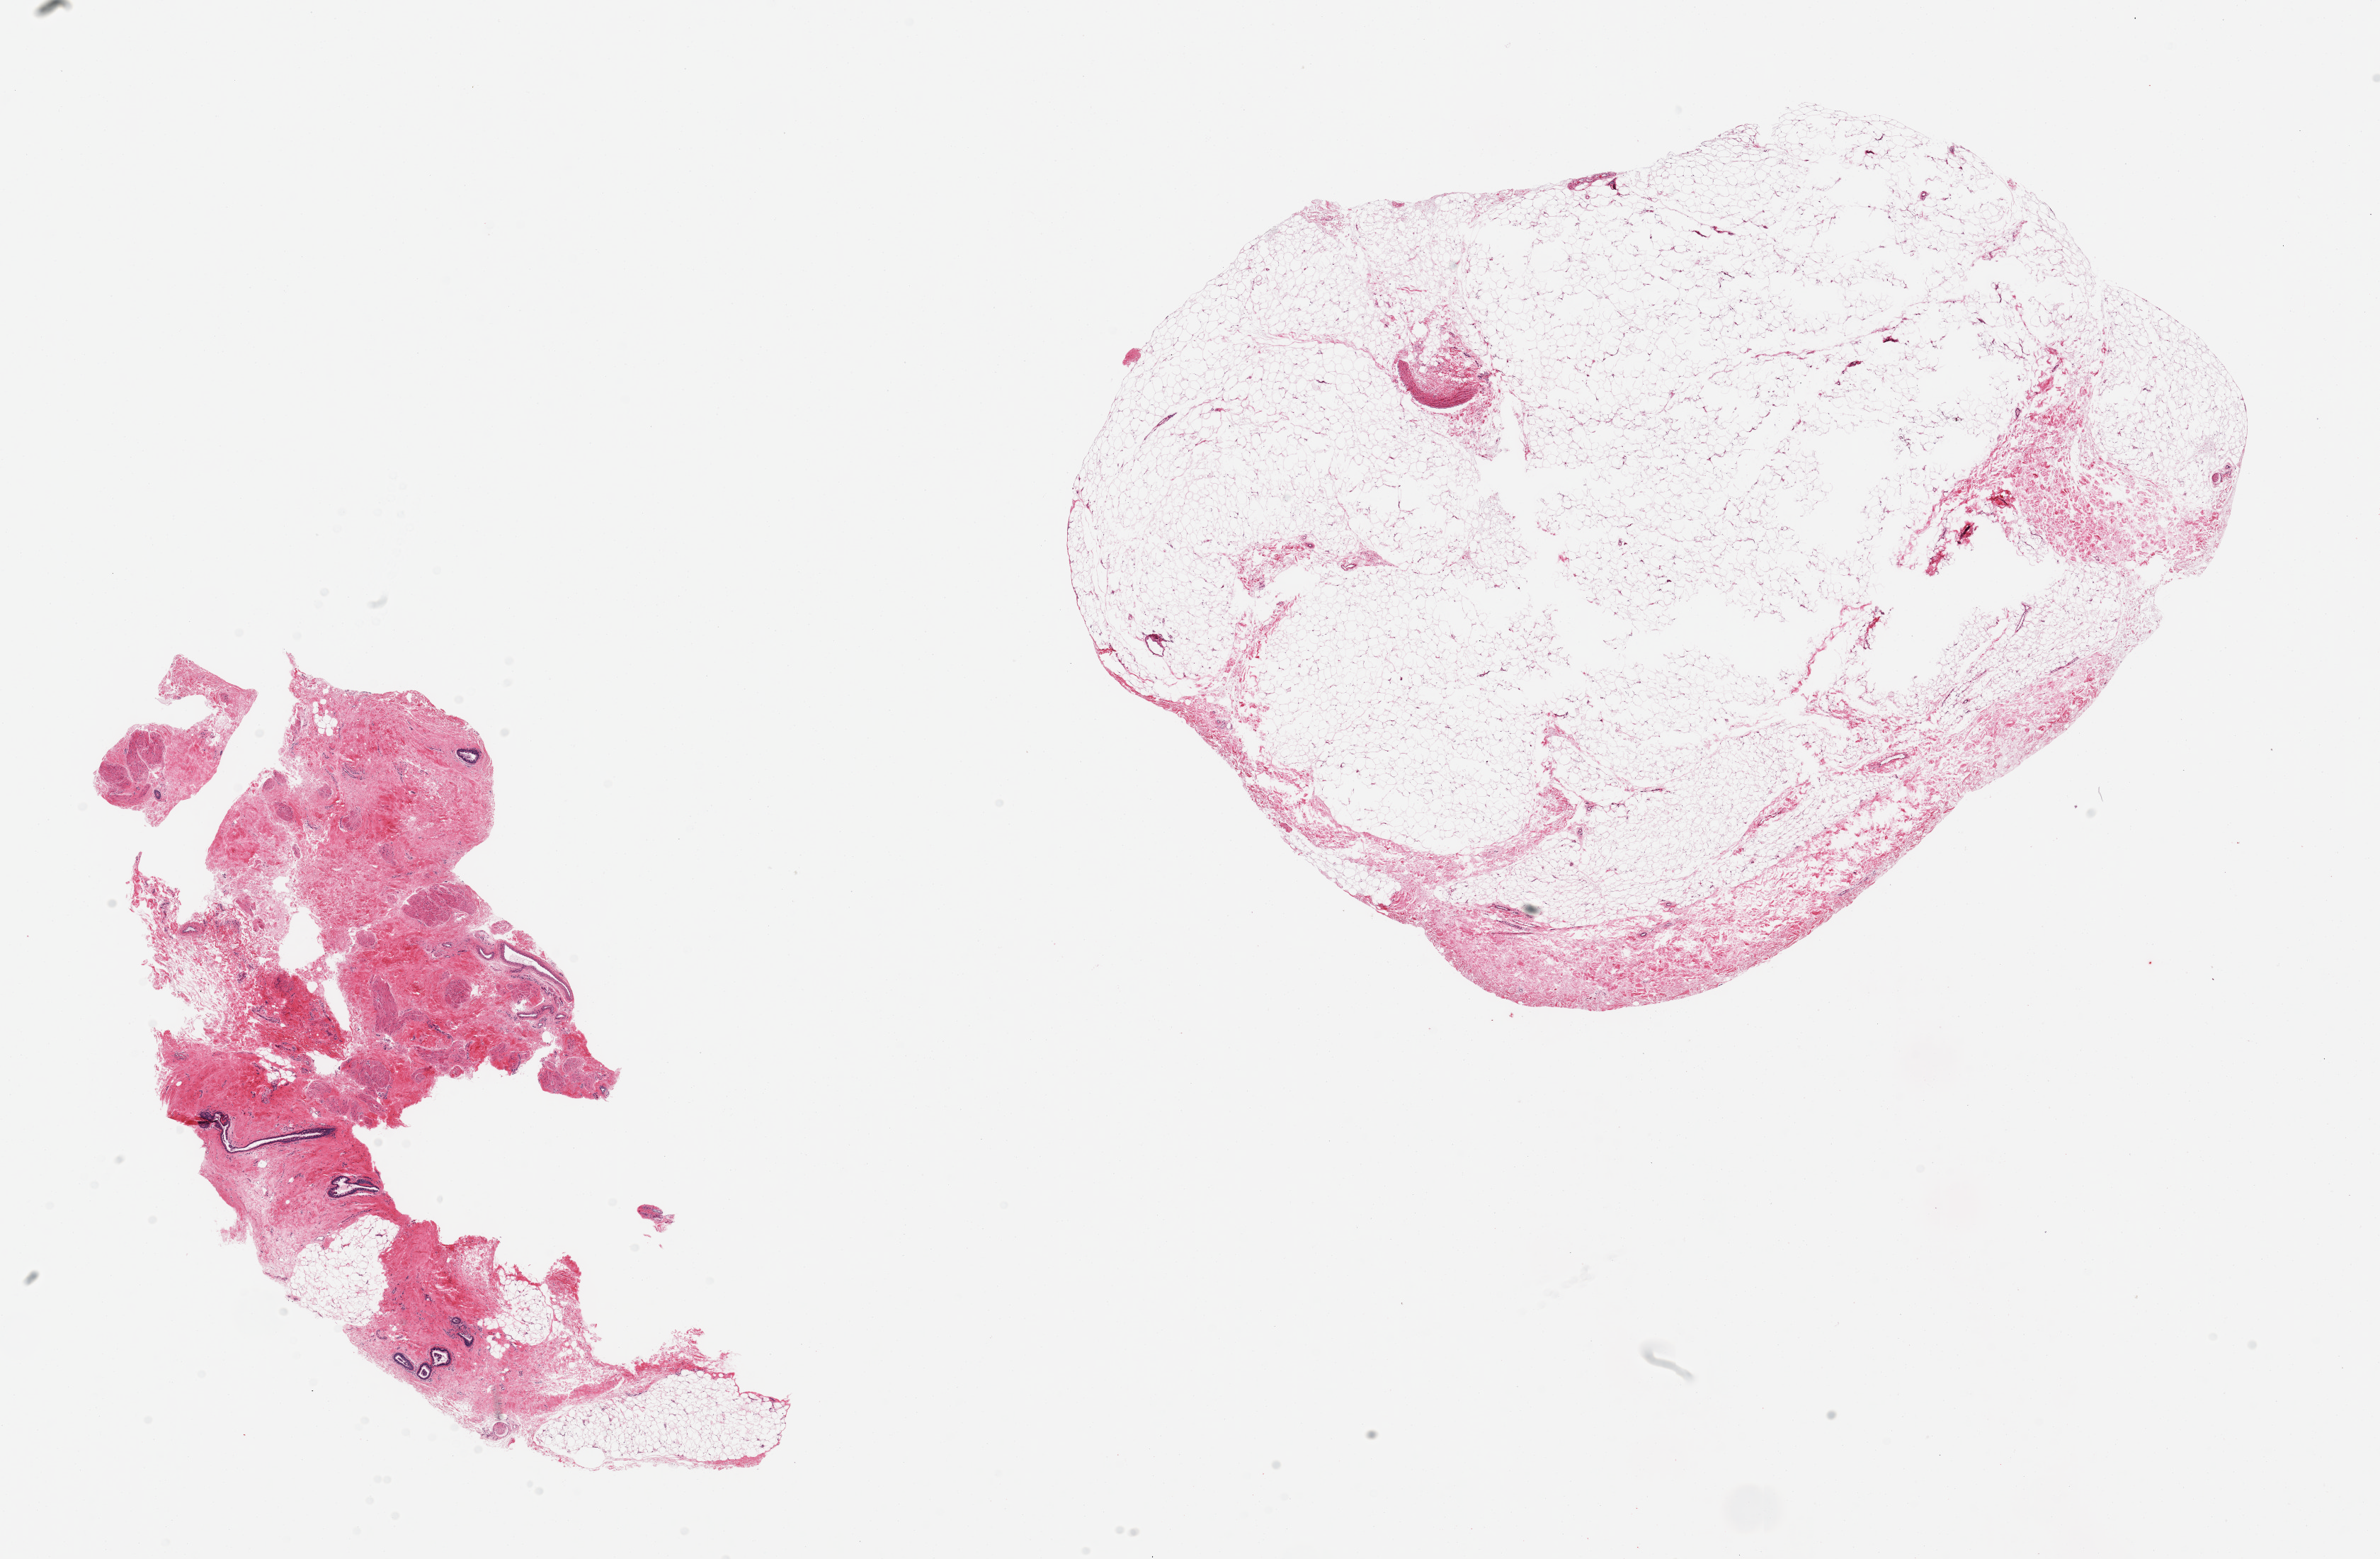
Digitized haematoxylin and eosin-stained section, brightfield — shown as a low-resolution overview of the whole scanned area (about 26.6 x 17.4 mm). PAXgene-fixed paraffin-embedded (PFPE) section. Target tissue: breast. Tissue donor sample. Male donor.
• pathologist's review note for this sample: 2 pieces; 1 is predominantly fat with <10% fibrous component, 2nd is predominantly stroma with scattered ducts with mild hyperplasia, bundles of smooth muscle, and ~15% fat